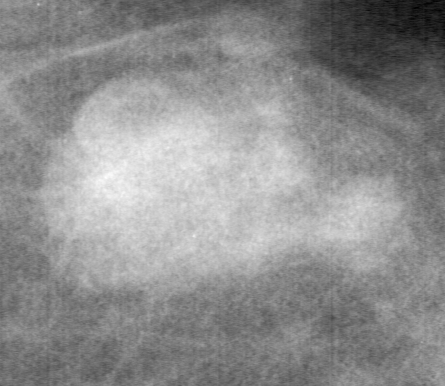
Crop from a digitized film mammogram around one marked abnormality, right breast, CC view, BI-RADS breast density category 2 (scale 1–4).
- Mass, shape lobulated, margins circumscribed; BI-RADS assessment category 4; pathology result (as recorded, not read from the image): benign.